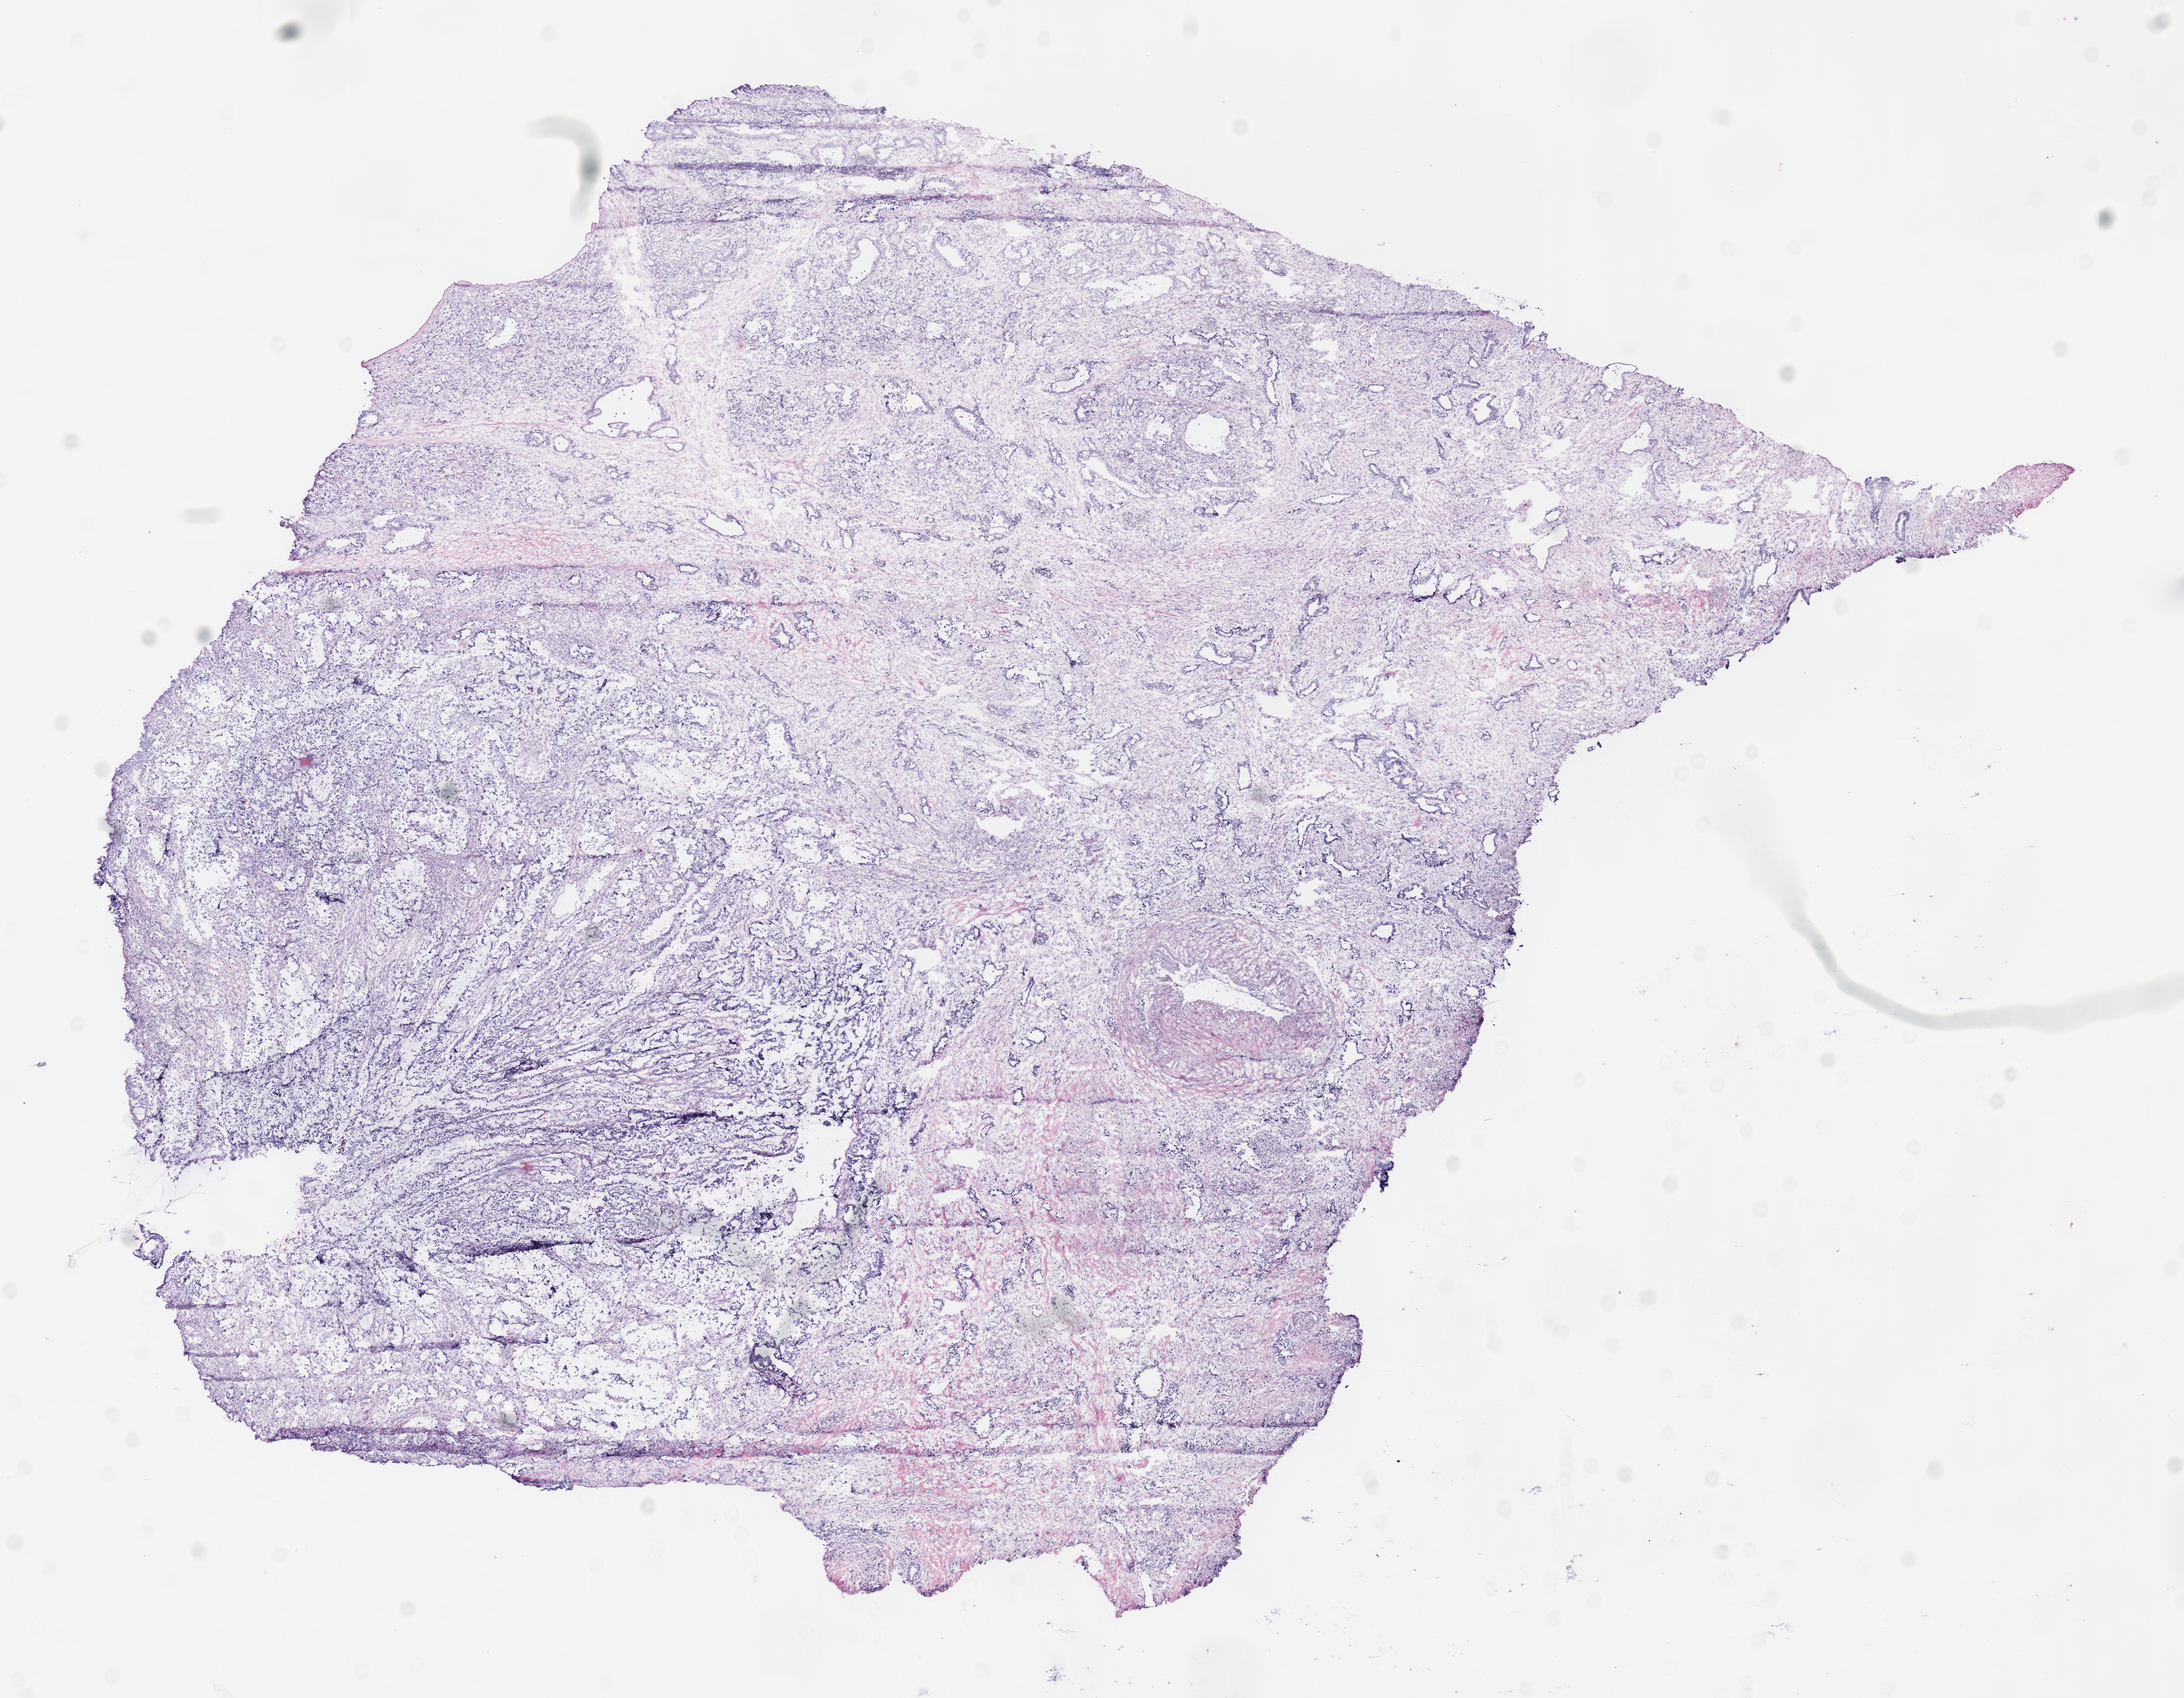
H&E whole-slide image, whole scanned area (about 12.2 x 9.5 mm, acquisition: 40x scan) shown as a low-resolution overview, frozen section from the top of the tissue portion, primary tumour sample from the pancreas. Male, age 80 years at initial diagnosis. Histologic grade: G3 (poorly differentiated). Pathologist review of this section (percent, as recorded): tumour cells 75%, tumour nuclei 75%, normal cells 0%, stromal cells 25%, necrosis 0%.
Histologic diagnosis: Infiltrating duct carcinoma, NOS. Lymph nodes positive (case pathology): 4 of 11 examined. AJCC pathologic stage: IIB.